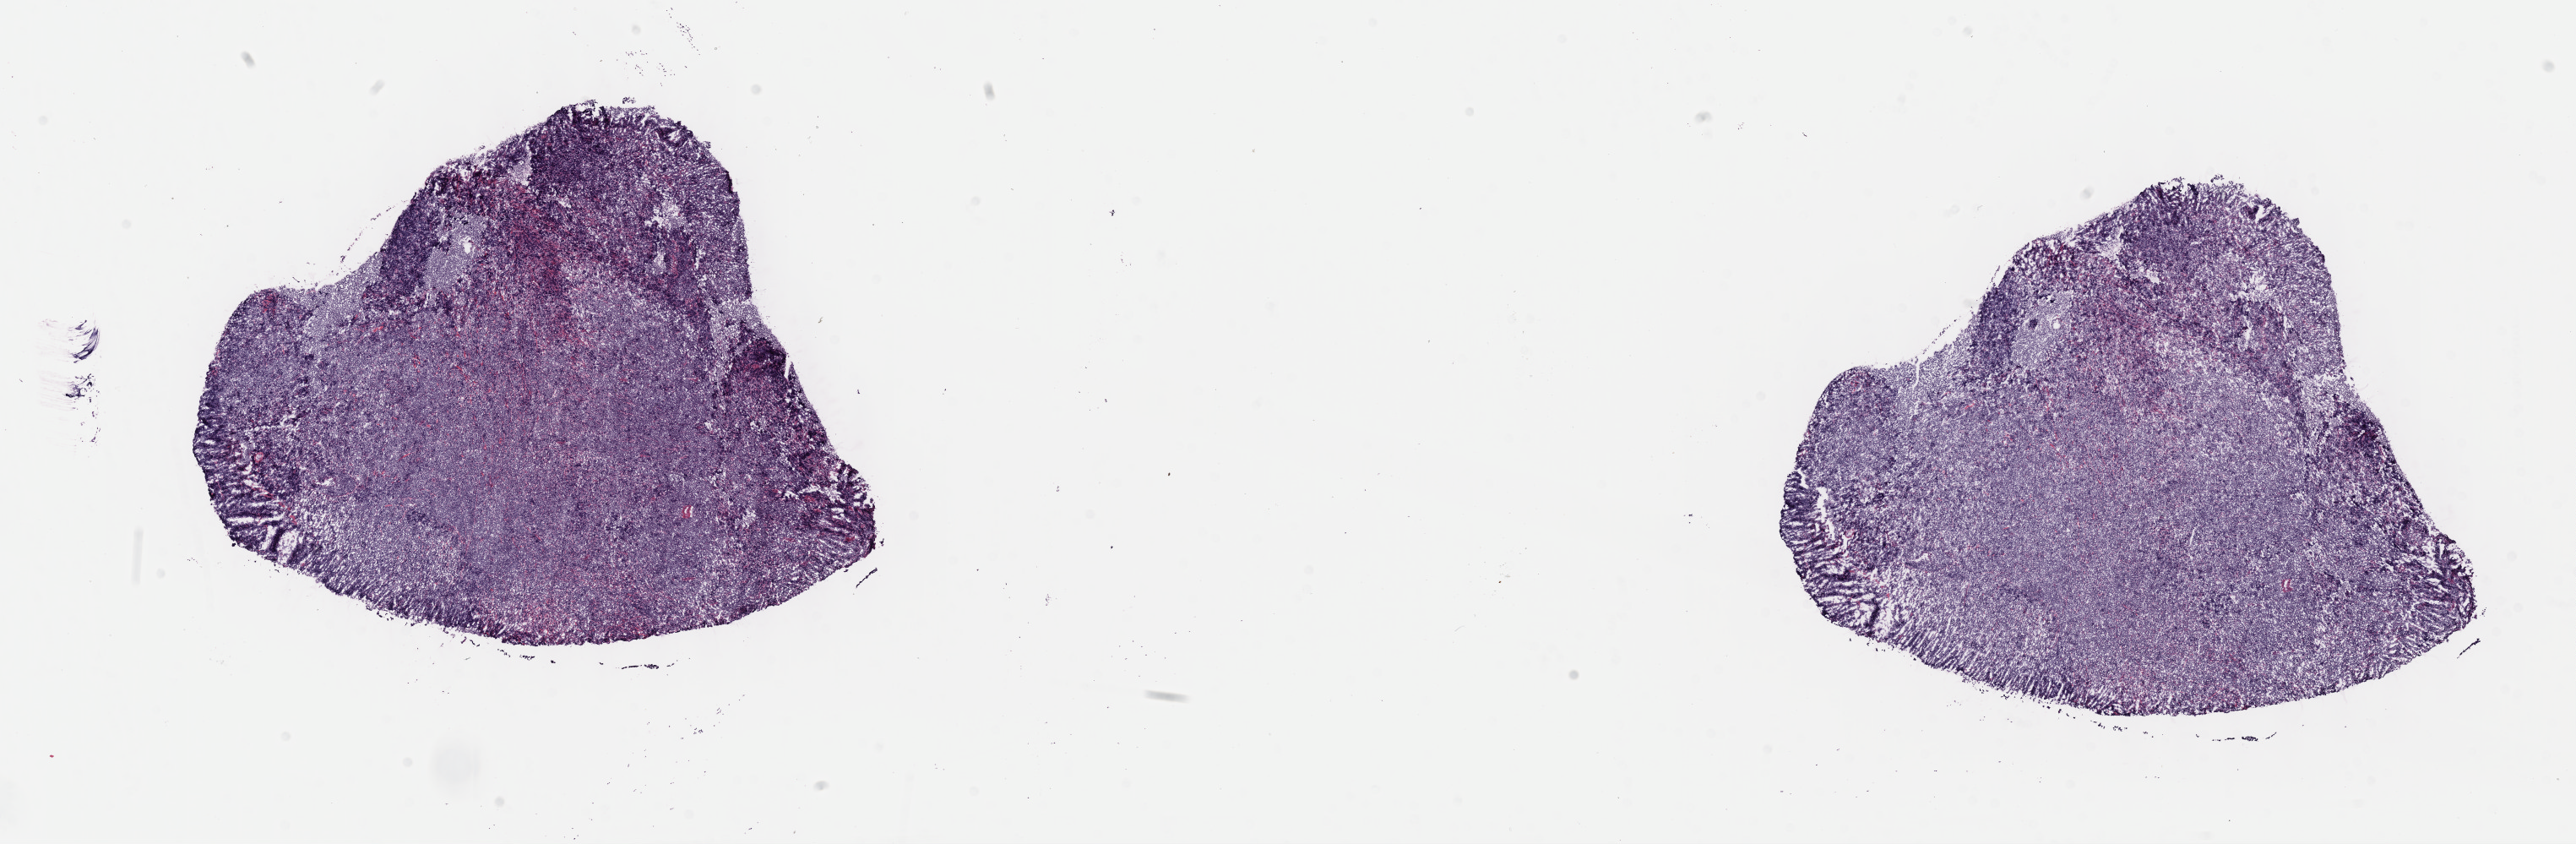
Whole-slide image, haematoxylin and eosin stain — shown as a low-resolution overview of the whole scanned area (about 24.7 x 8.1 mm), frozen section, specimen: primary tumor, anatomic site: mandible. Male patient, 11 years old. Composition of this section per pathologist review: tumor cells 95%, tumor nuclei 95%, stromal cells 3%, necrosis 2%, normal cells 0%. Infiltration values recorded for this section: lymphocyte infiltration 3%, monocyte infiltration 5%, neutrophil infiltration 0%.
• histologic diagnosis: Burkitt lymphoma, NOS
• Ann Arbor stage (patient): Stage III